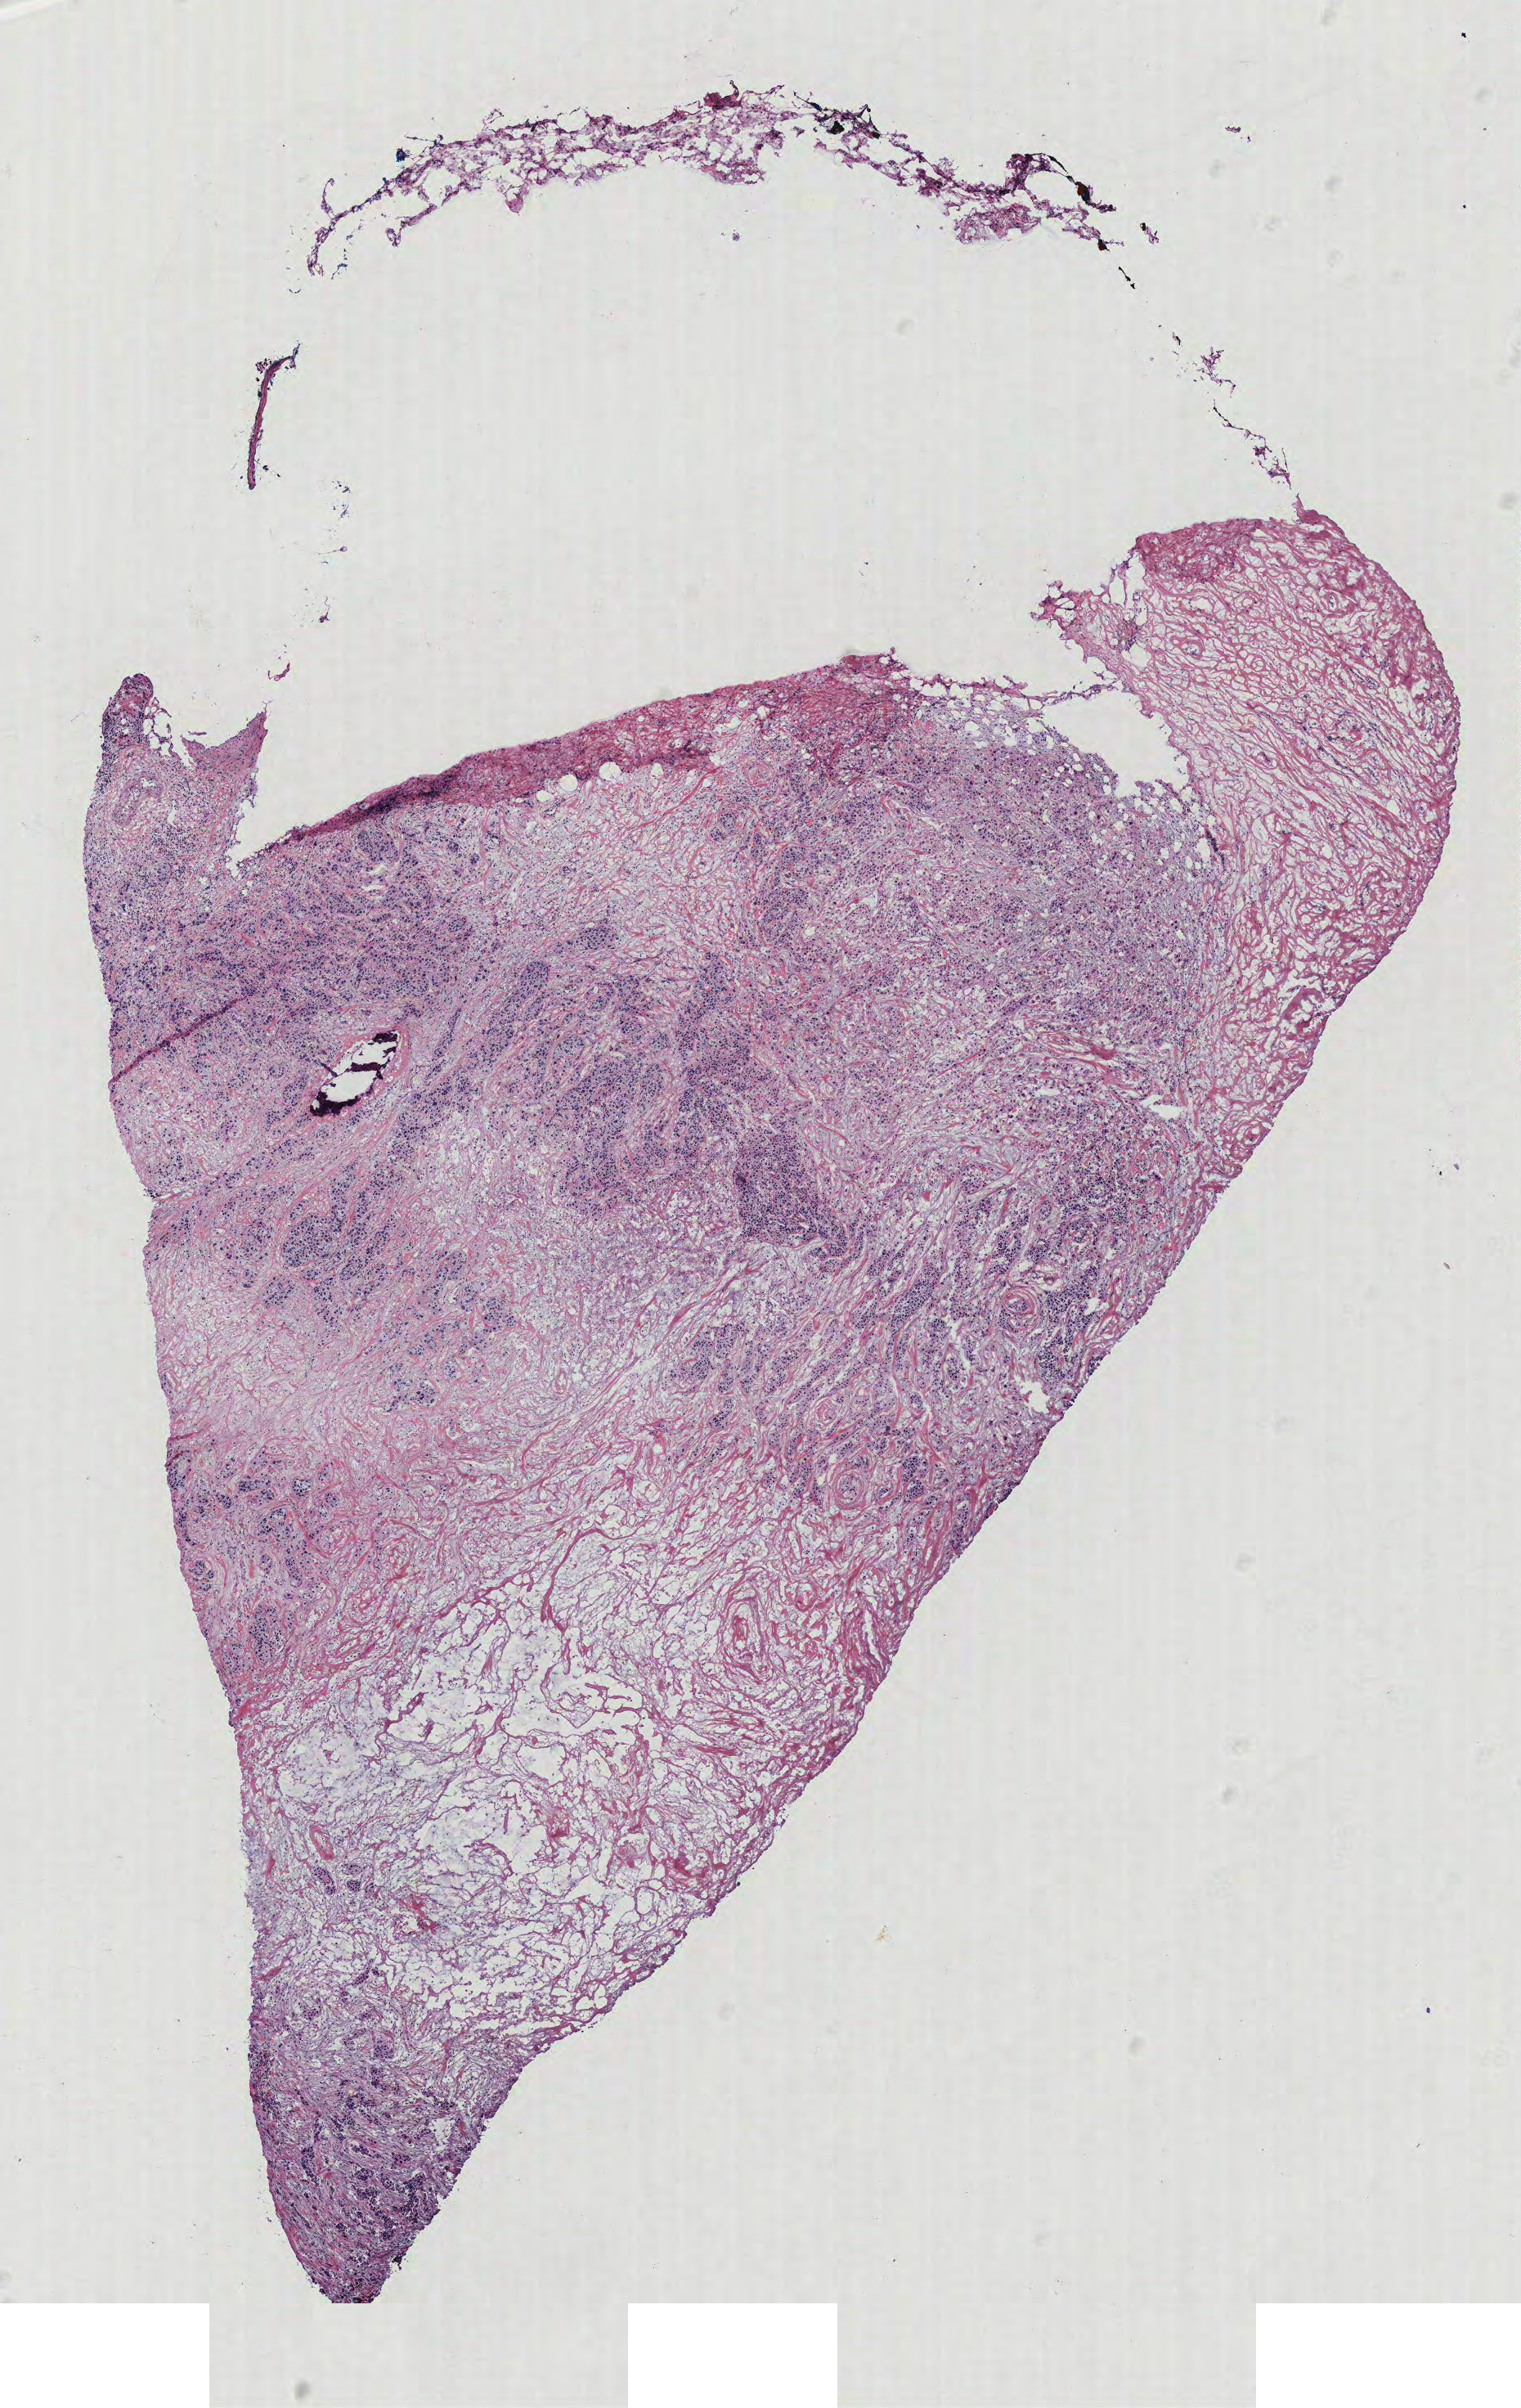
Whole-slide histology image, Hematoxylin and eosin (H&E) stained — low-resolution overview of the scanned area, about 7.4 x 11.8 mm (from a 40x scan). Breast, tissue type not recorded.
- patient diagnosis (cohort enrolment): breast cancer (breast)